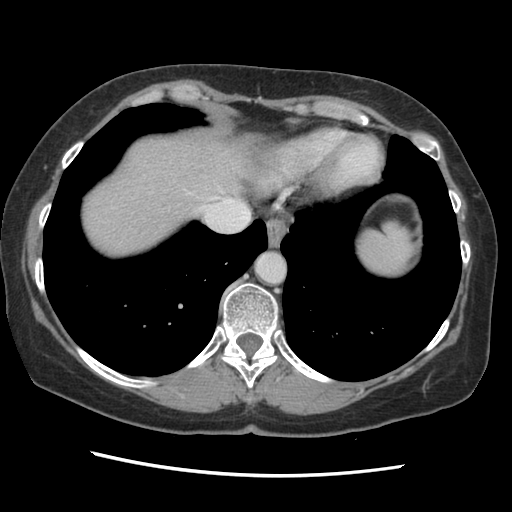
Contrast-enhanced abdominal CT, one axial slice. Position 122 of 141 along the scan axis. 120 kVp. Soft-tissue window (W 400 / L 40 HU). 512 × 512 image matrix. Female patient, age 61 years. Case-level facts recorded for this patient, not image findings: diagnosis: colorectal cancer liver metastases, imaged before liver resection; multiple liver metastases: no.
Structures marked on this image (expert manual segmentation):
- hepatic veins: box from (x=202, y=187) to (x=232, y=213) px
- liver: (x=80, y=134)–(x=252, y=257)
- planned liver remnant (the part of the liver to remain after resection): (x=81, y=134)–(x=251, y=258)